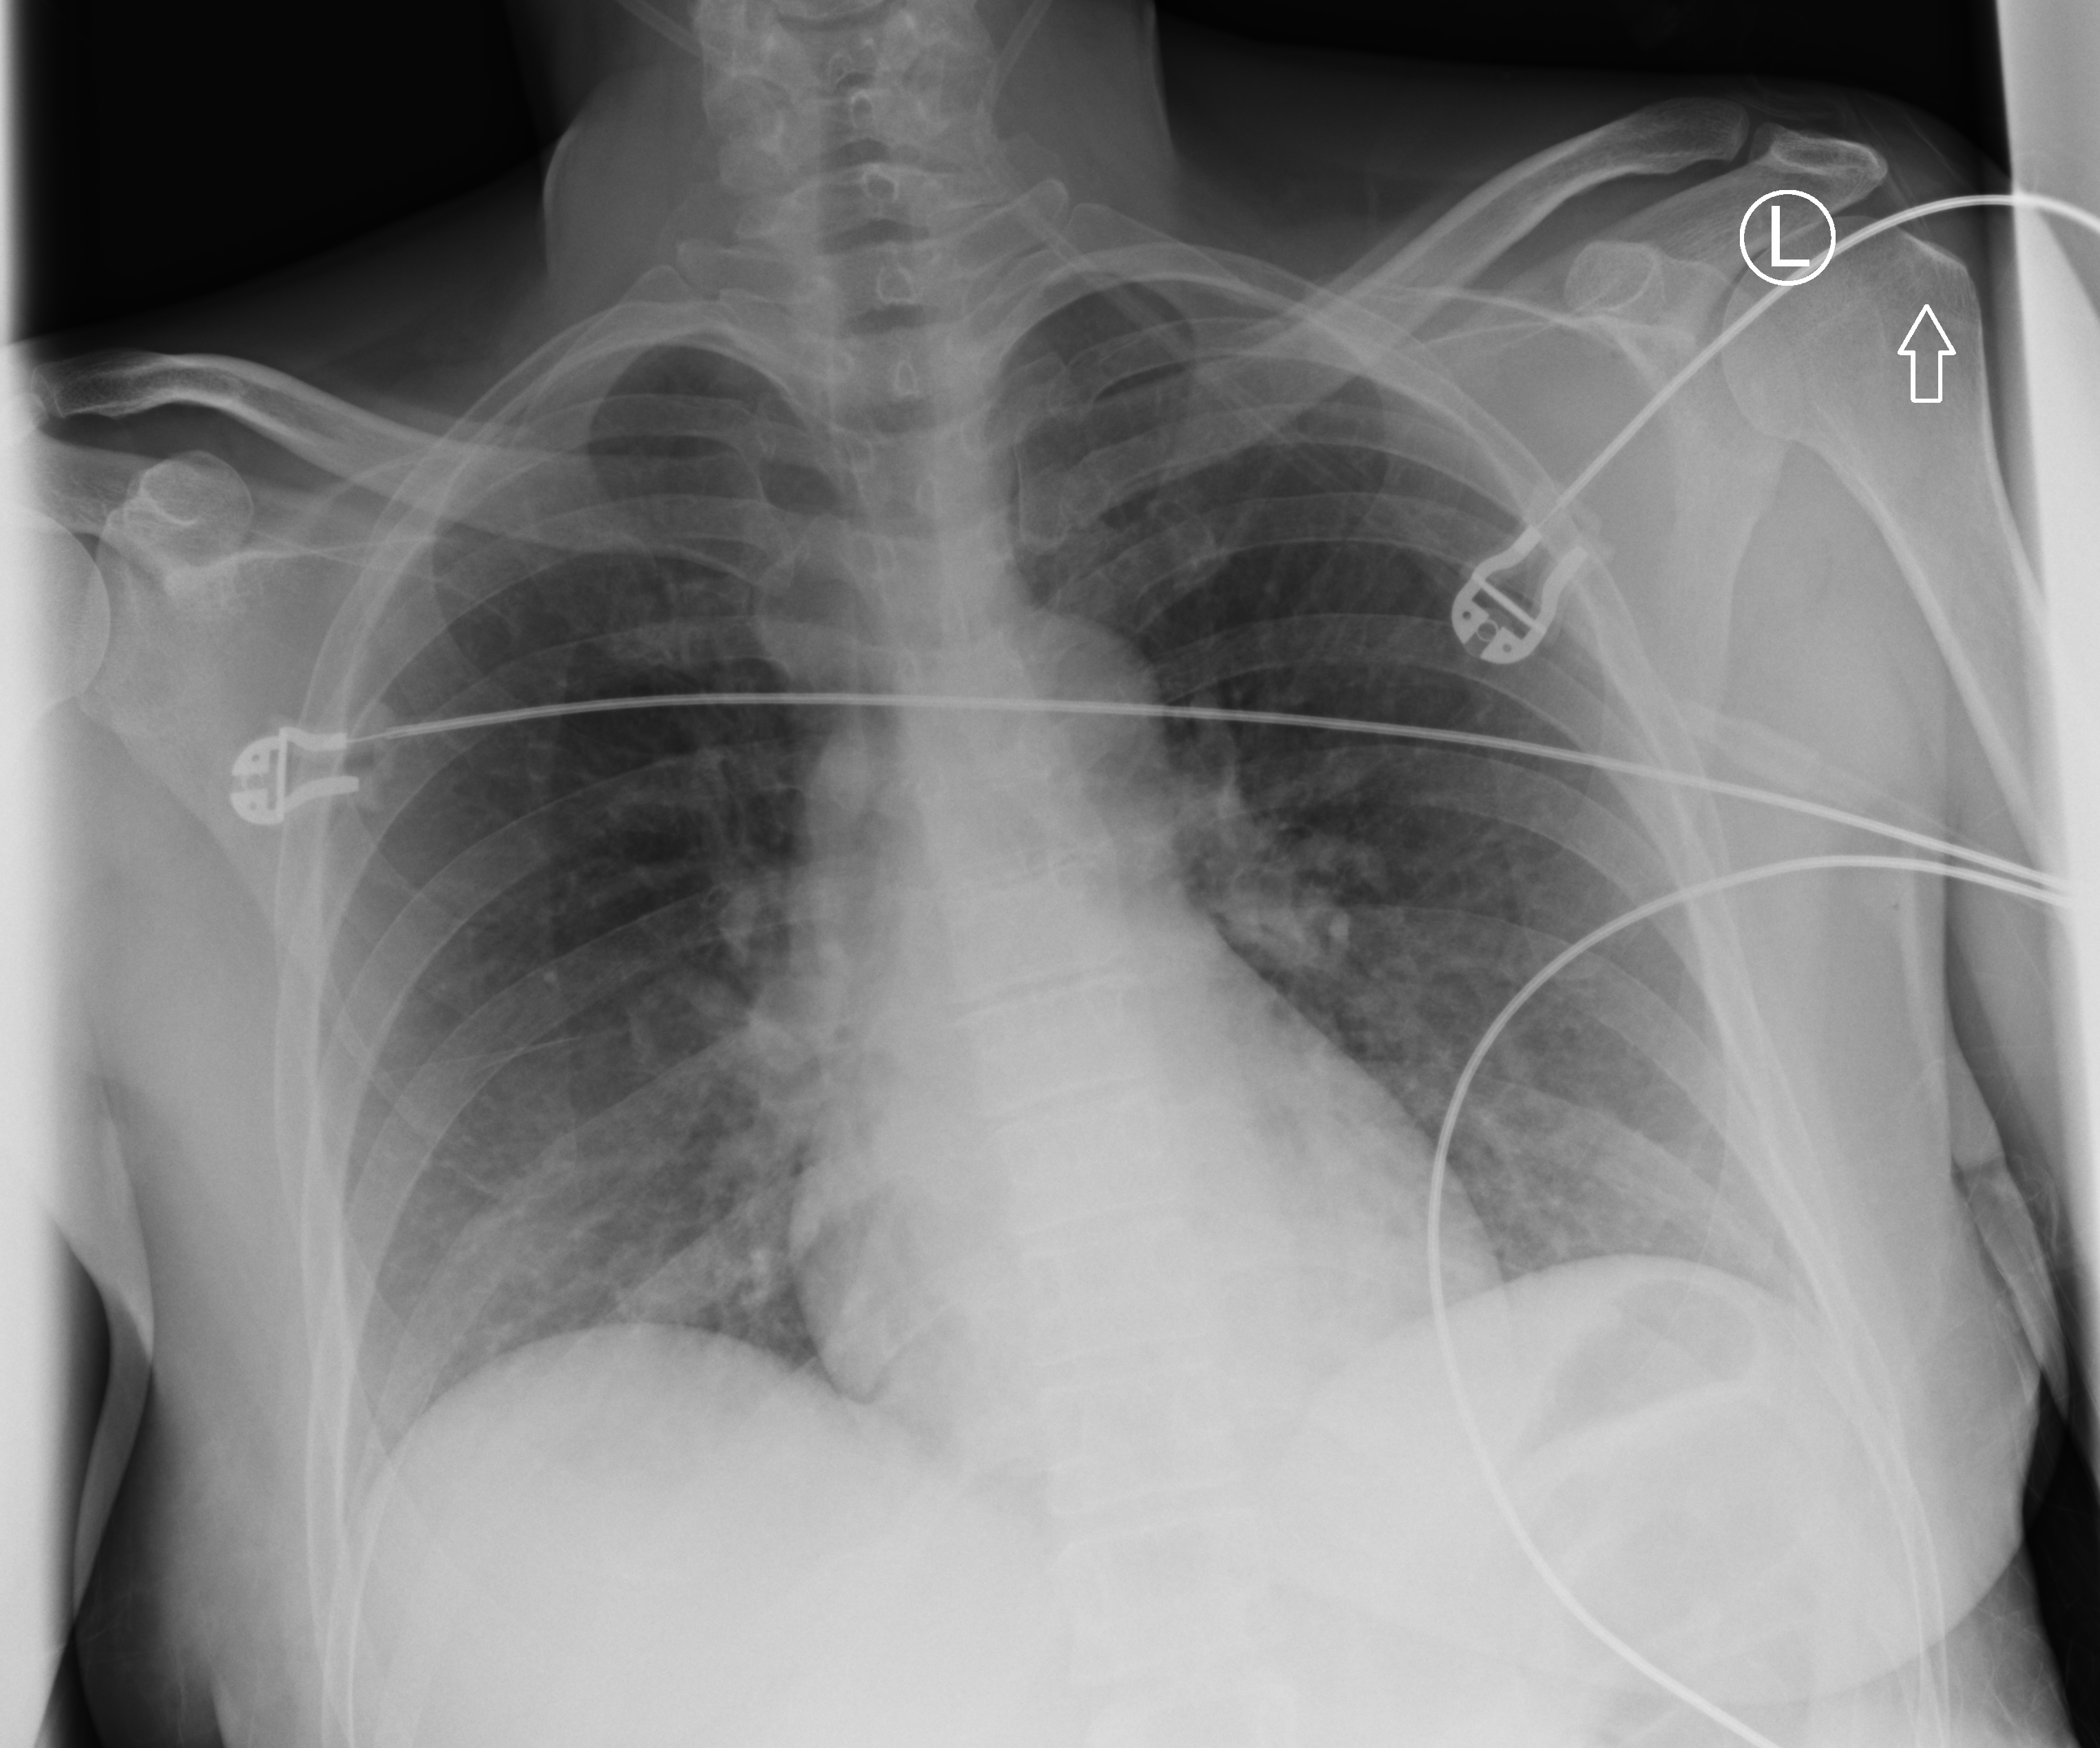
Portable chest radiograph, anteroposterior (AP) projection. Patient hospitalised with COVID-19; female, aged 18–59 years.
Hospital-stay facts (about this admission, not read from this image; timing relative to this image not recorded): mechanically ventilated during this hospital stay: no; admitted to intensive care during this hospital stay: yes; diabetes (admission record): no.